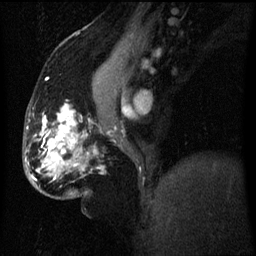
Breast MRI (dynamic contrast-enhanced), one sagittal slice; position 29 of 60 along the scan axis; dynamic contrast-enhanced series, image 2 of 3 at this slice position (ordered by acquisition); 1.5 T; TE 4.2 ms, TR 8 ms; 256 × 256 image matrix, field of view 200 × 200 mm. Patient: female, 50 years.
Structures marked on this image (semi-automatically segmented with operator editing):
- analysis volume of interest (the breast-tissue region the enhancement analysis was run in; not a lesion): bounding box (x1, y1, x2, y2) in pixels: (45, 136, 72, 179)
- tumour enhancement mask (voxels above the 70 % enhancement threshold inside the analysis volume of interest): (49, 150, 57, 159)